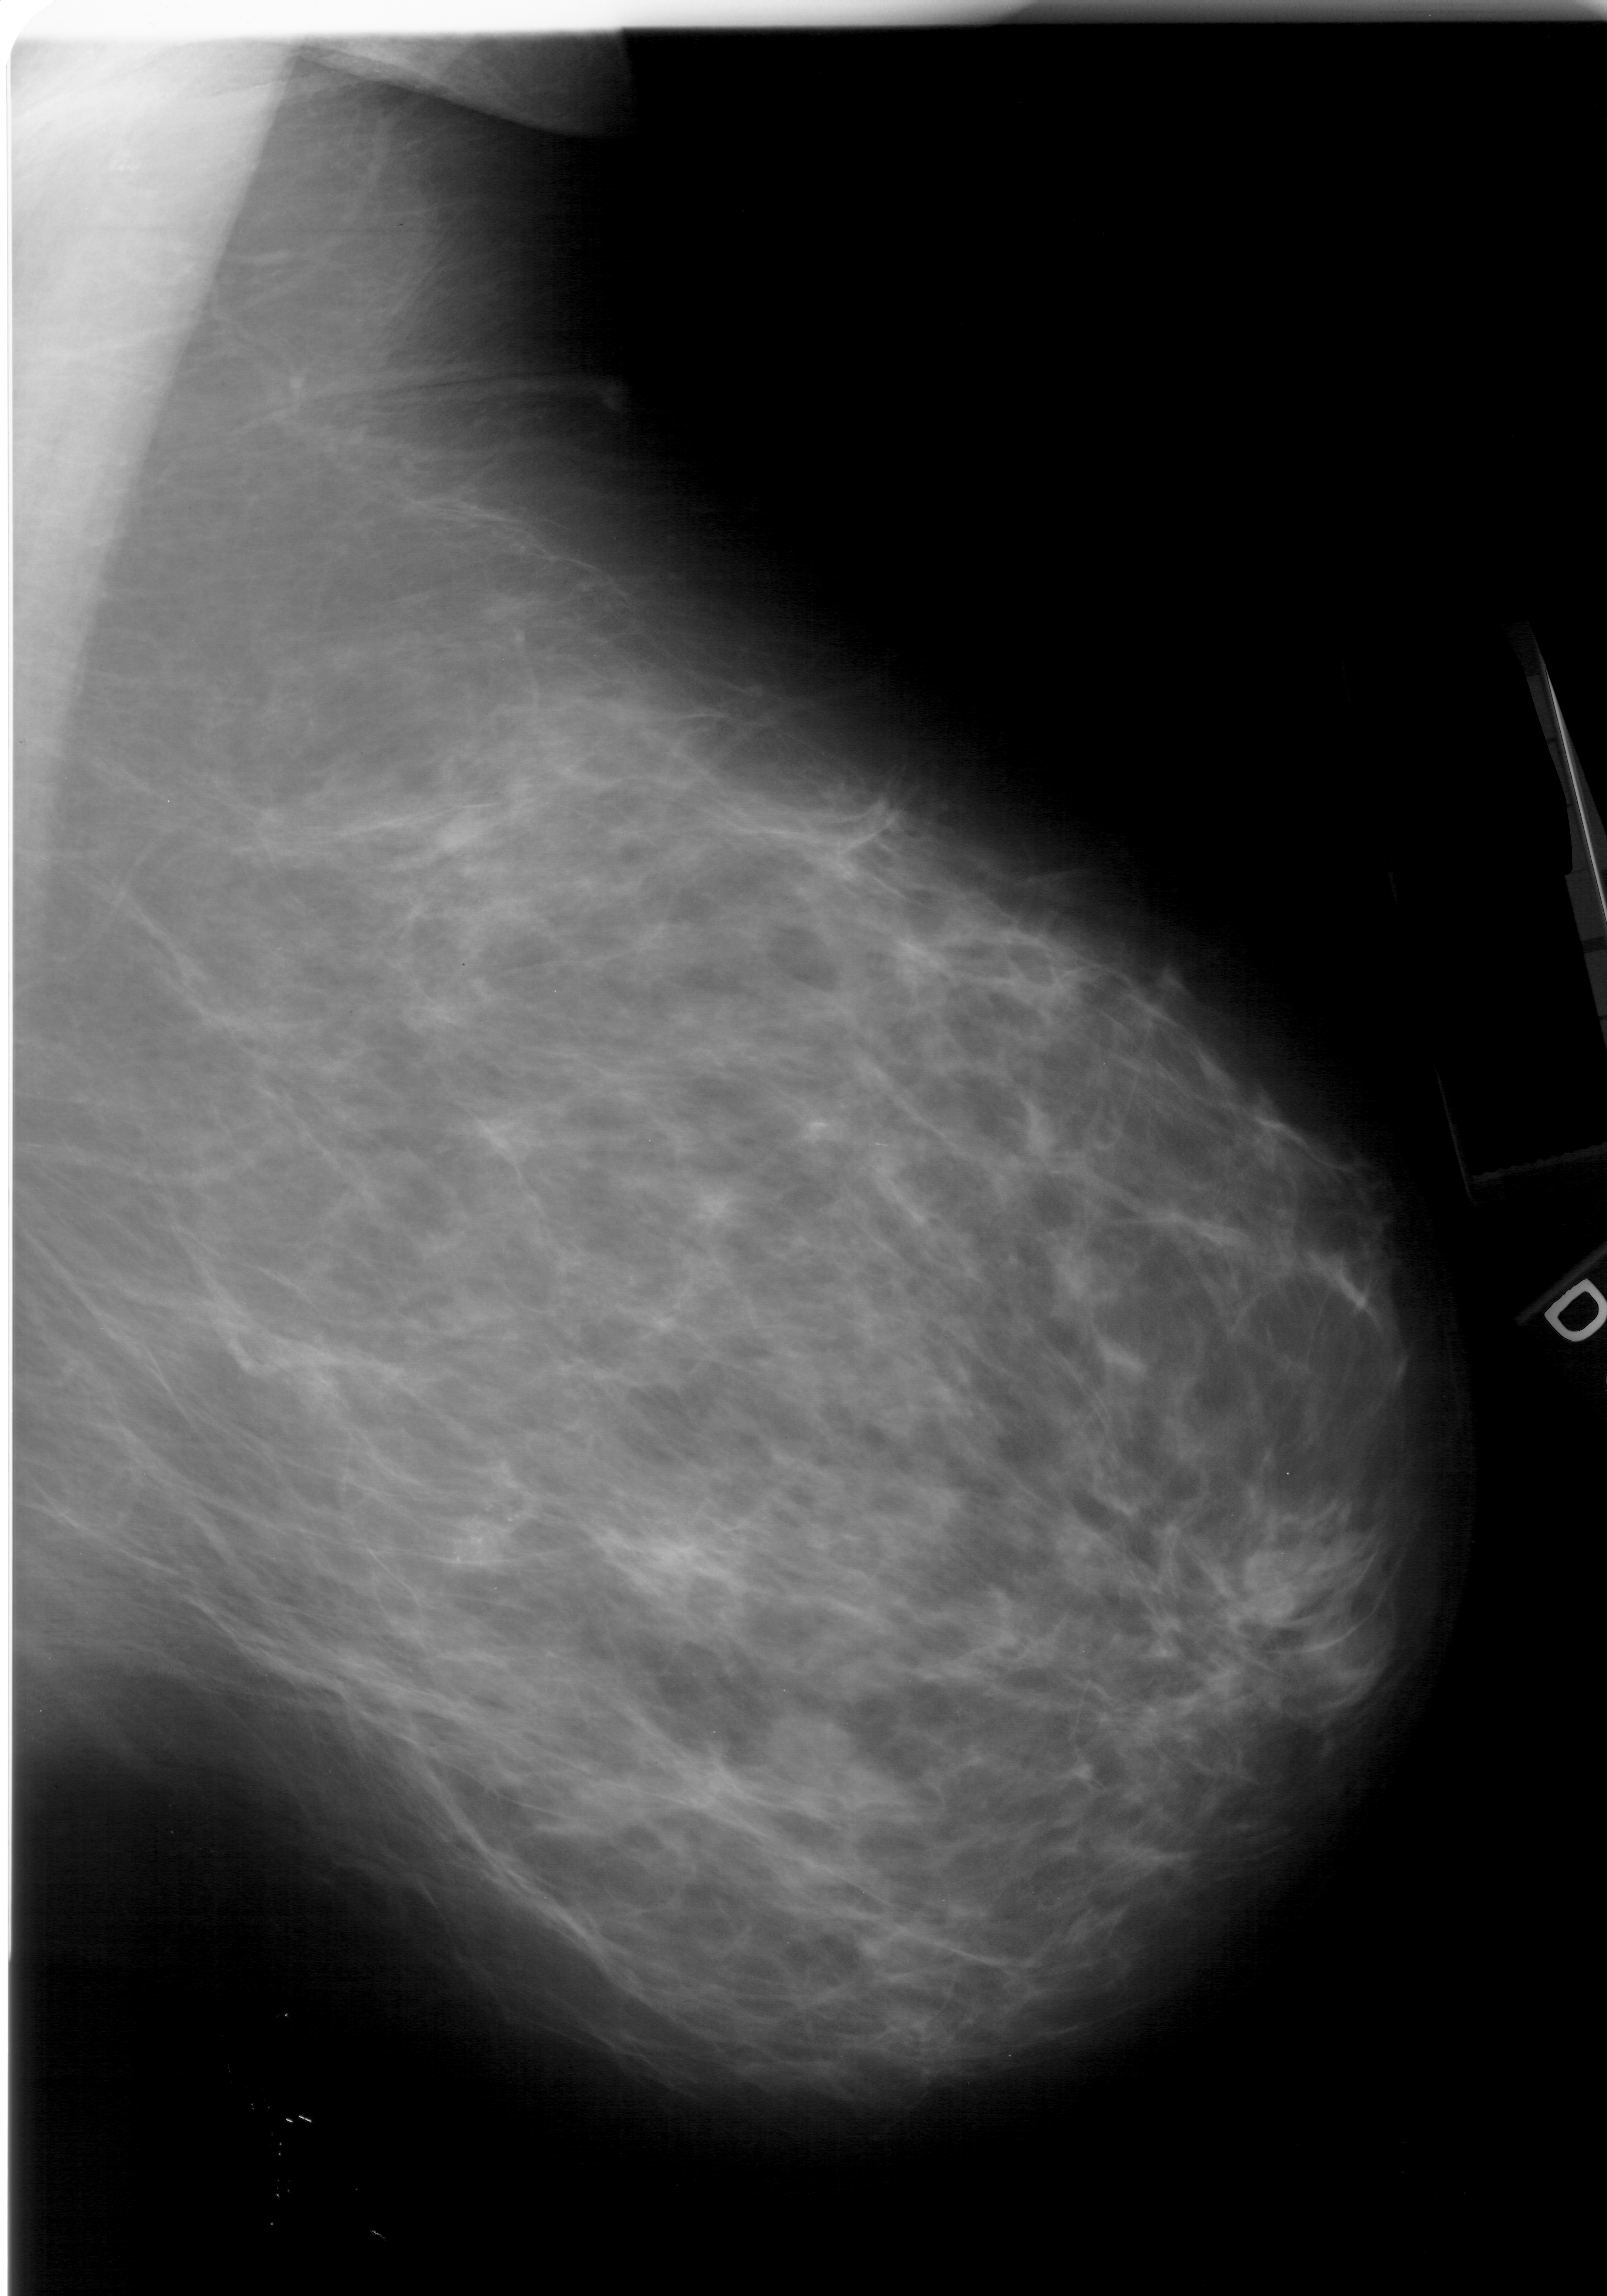
Scanned film-screen mammogram; right breast; mediolateral oblique (MLO) view.
- Abnormality record for this image: calcifications, morphology pleomorphic, distribution linear; BI-RADS assessment category 4; subtlety rating 3 on a 1 (subtle) to 5 (obvious) scale; pathology (as recorded): malignant.